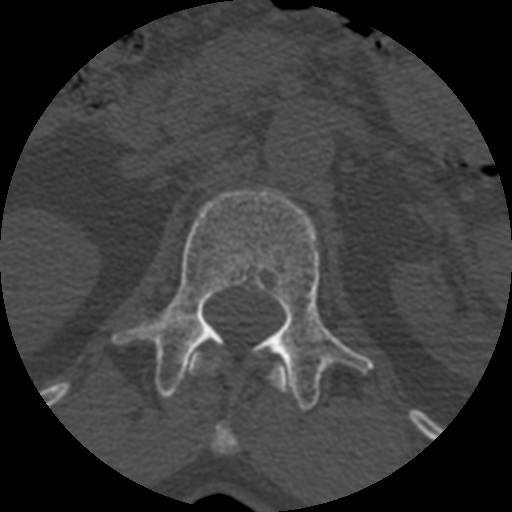
CT including the spine, one axial slice; slice 365 of 399 in the series (ordered by position); 120 kVp; bone window (W 1800 / L 400 HU); 512 × 512 image matrix, field of view 160 × 160 mm. Patient age 71 years. Case-level facts recorded for this patient, not image findings: primary cancer: prostate.
Annotated regions visible in this slice (semi-automatically segmented with operator editing):
- L1 vertebra: bounding box [x1, y1, x2, y2] px = [114, 187, 373, 409]
- T12 vertebra: [188, 353, 285, 455]